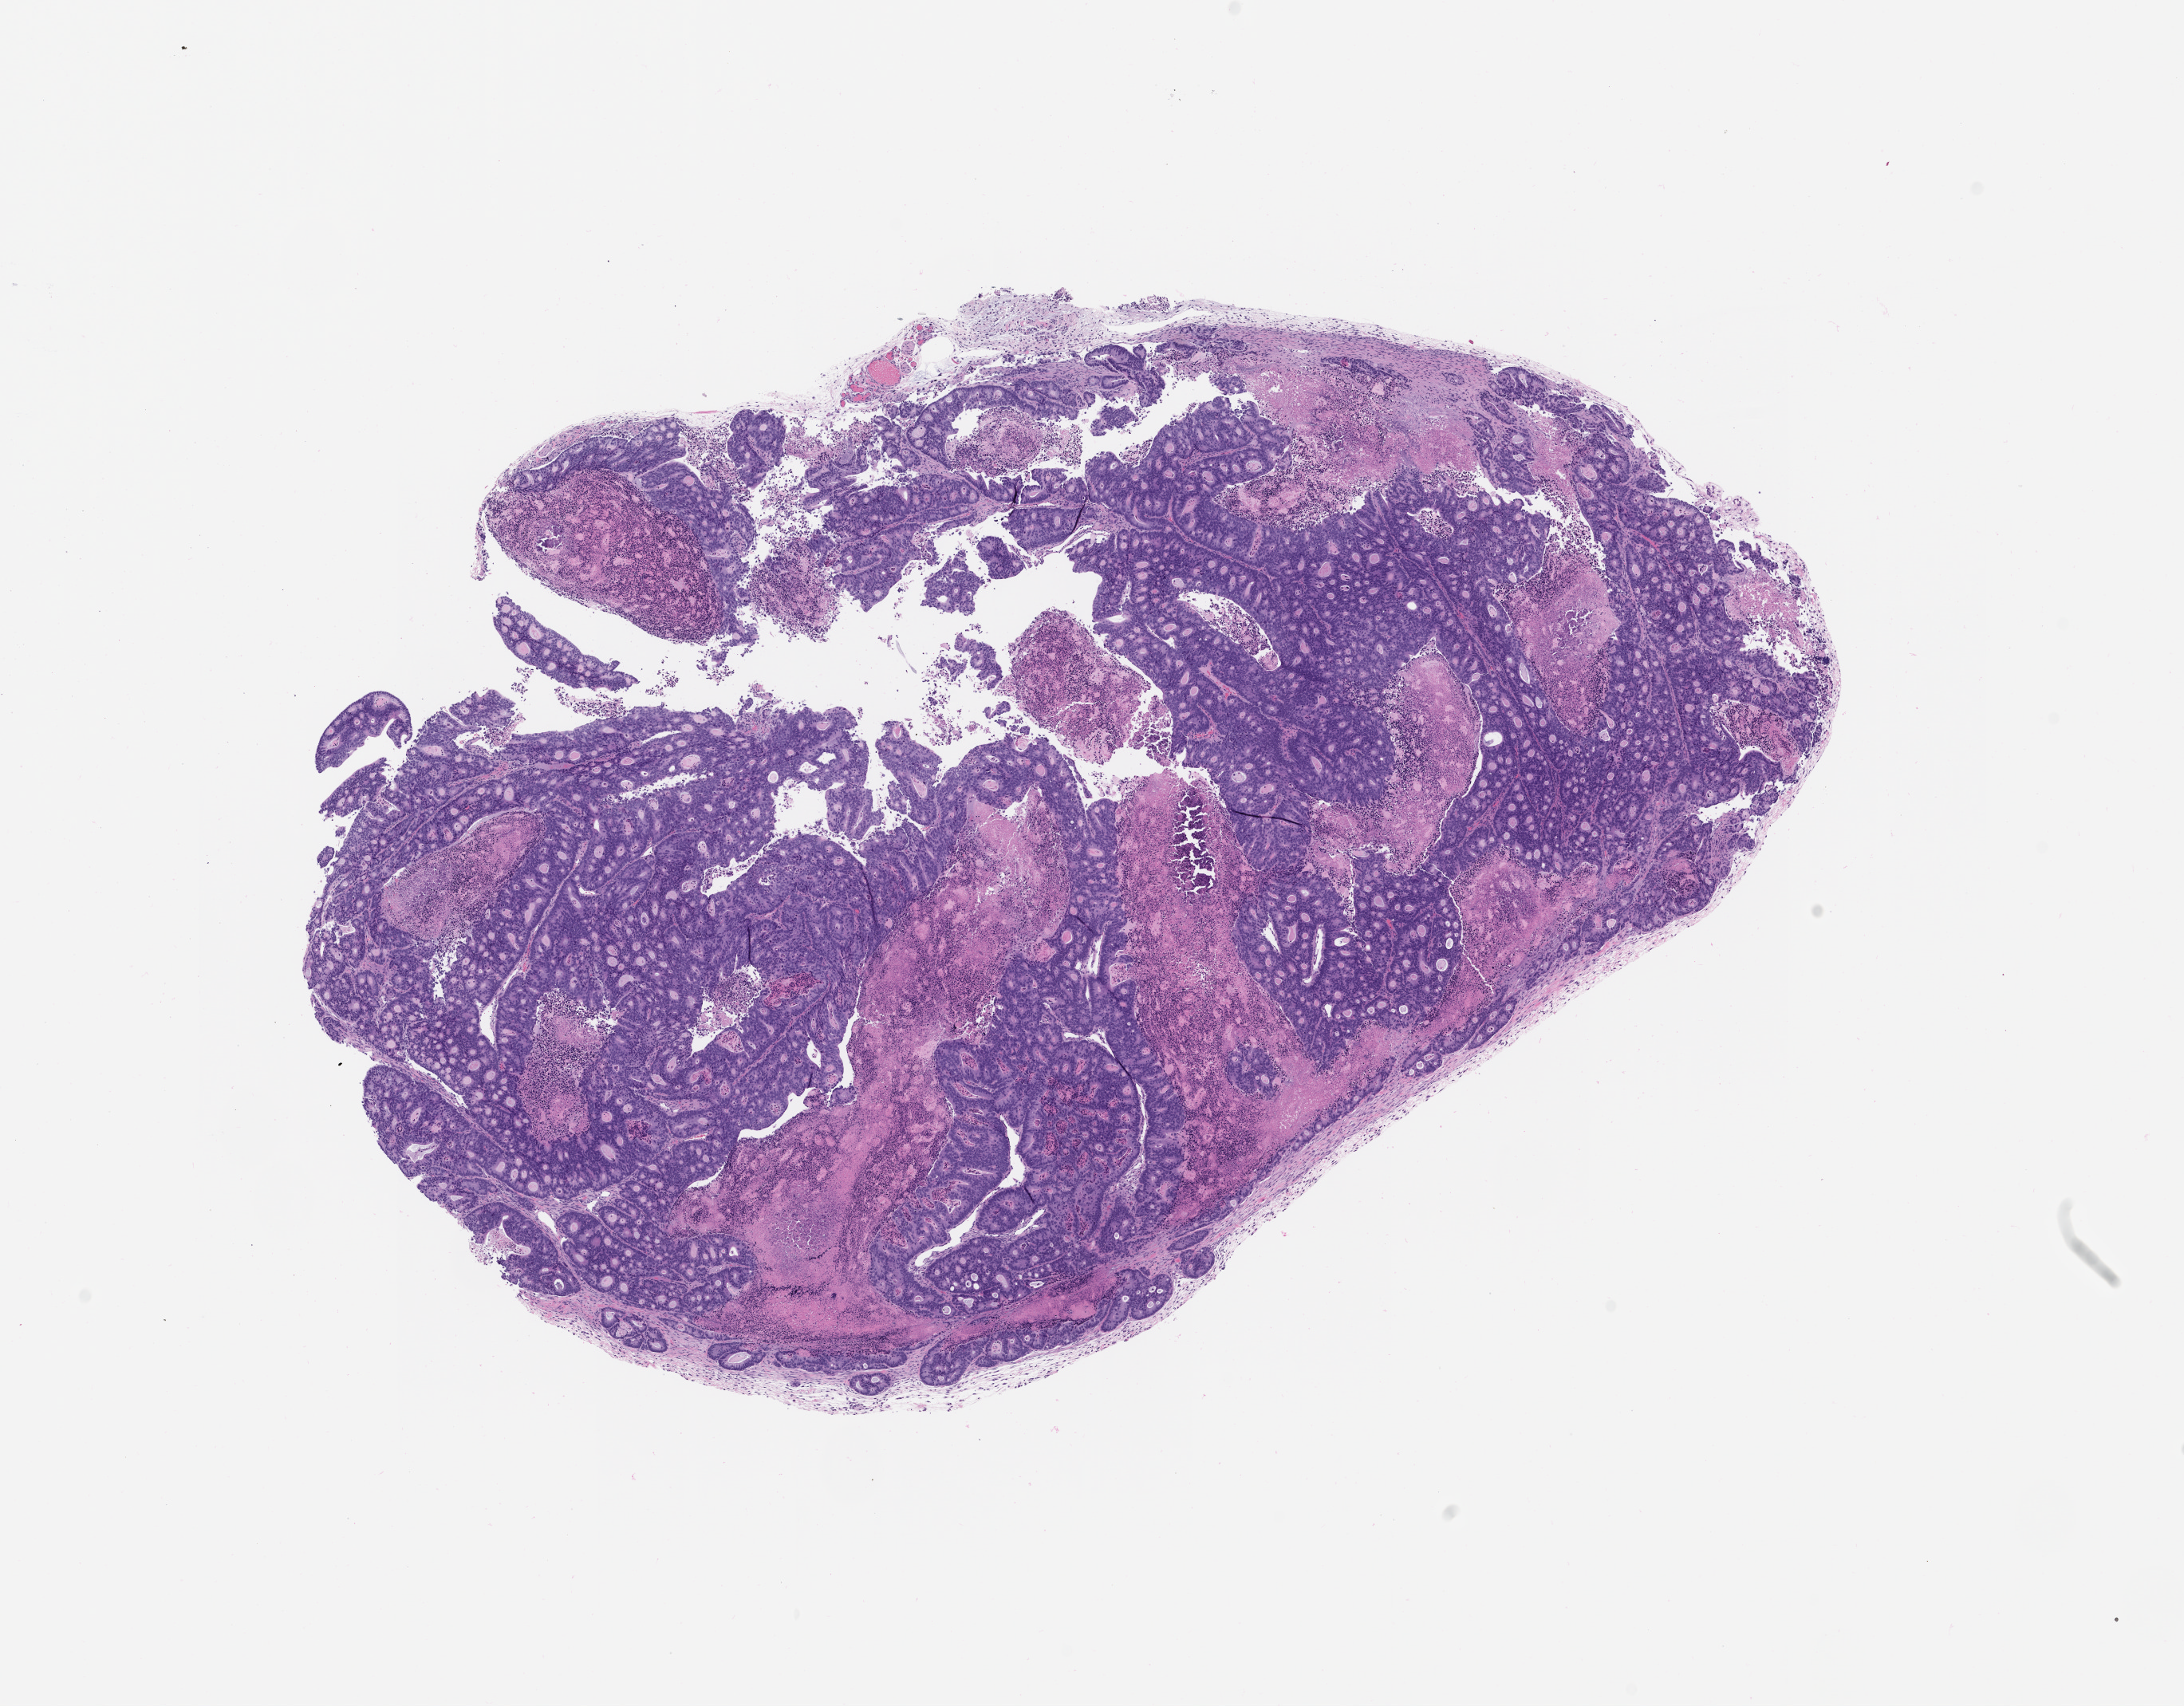
Whole-slide image, hematoxylin and eosin (H&E): patient-derived xenograft (human tumor grown in a mouse), passage 0, a low-resolution overview of the entire scanned area, about 11.0 x 8.6 mm; formalin-fixed paraffin-embedded section; originating tumor site category: colon.
Originating patient diagnosis: Colon Adenocarcinoma.